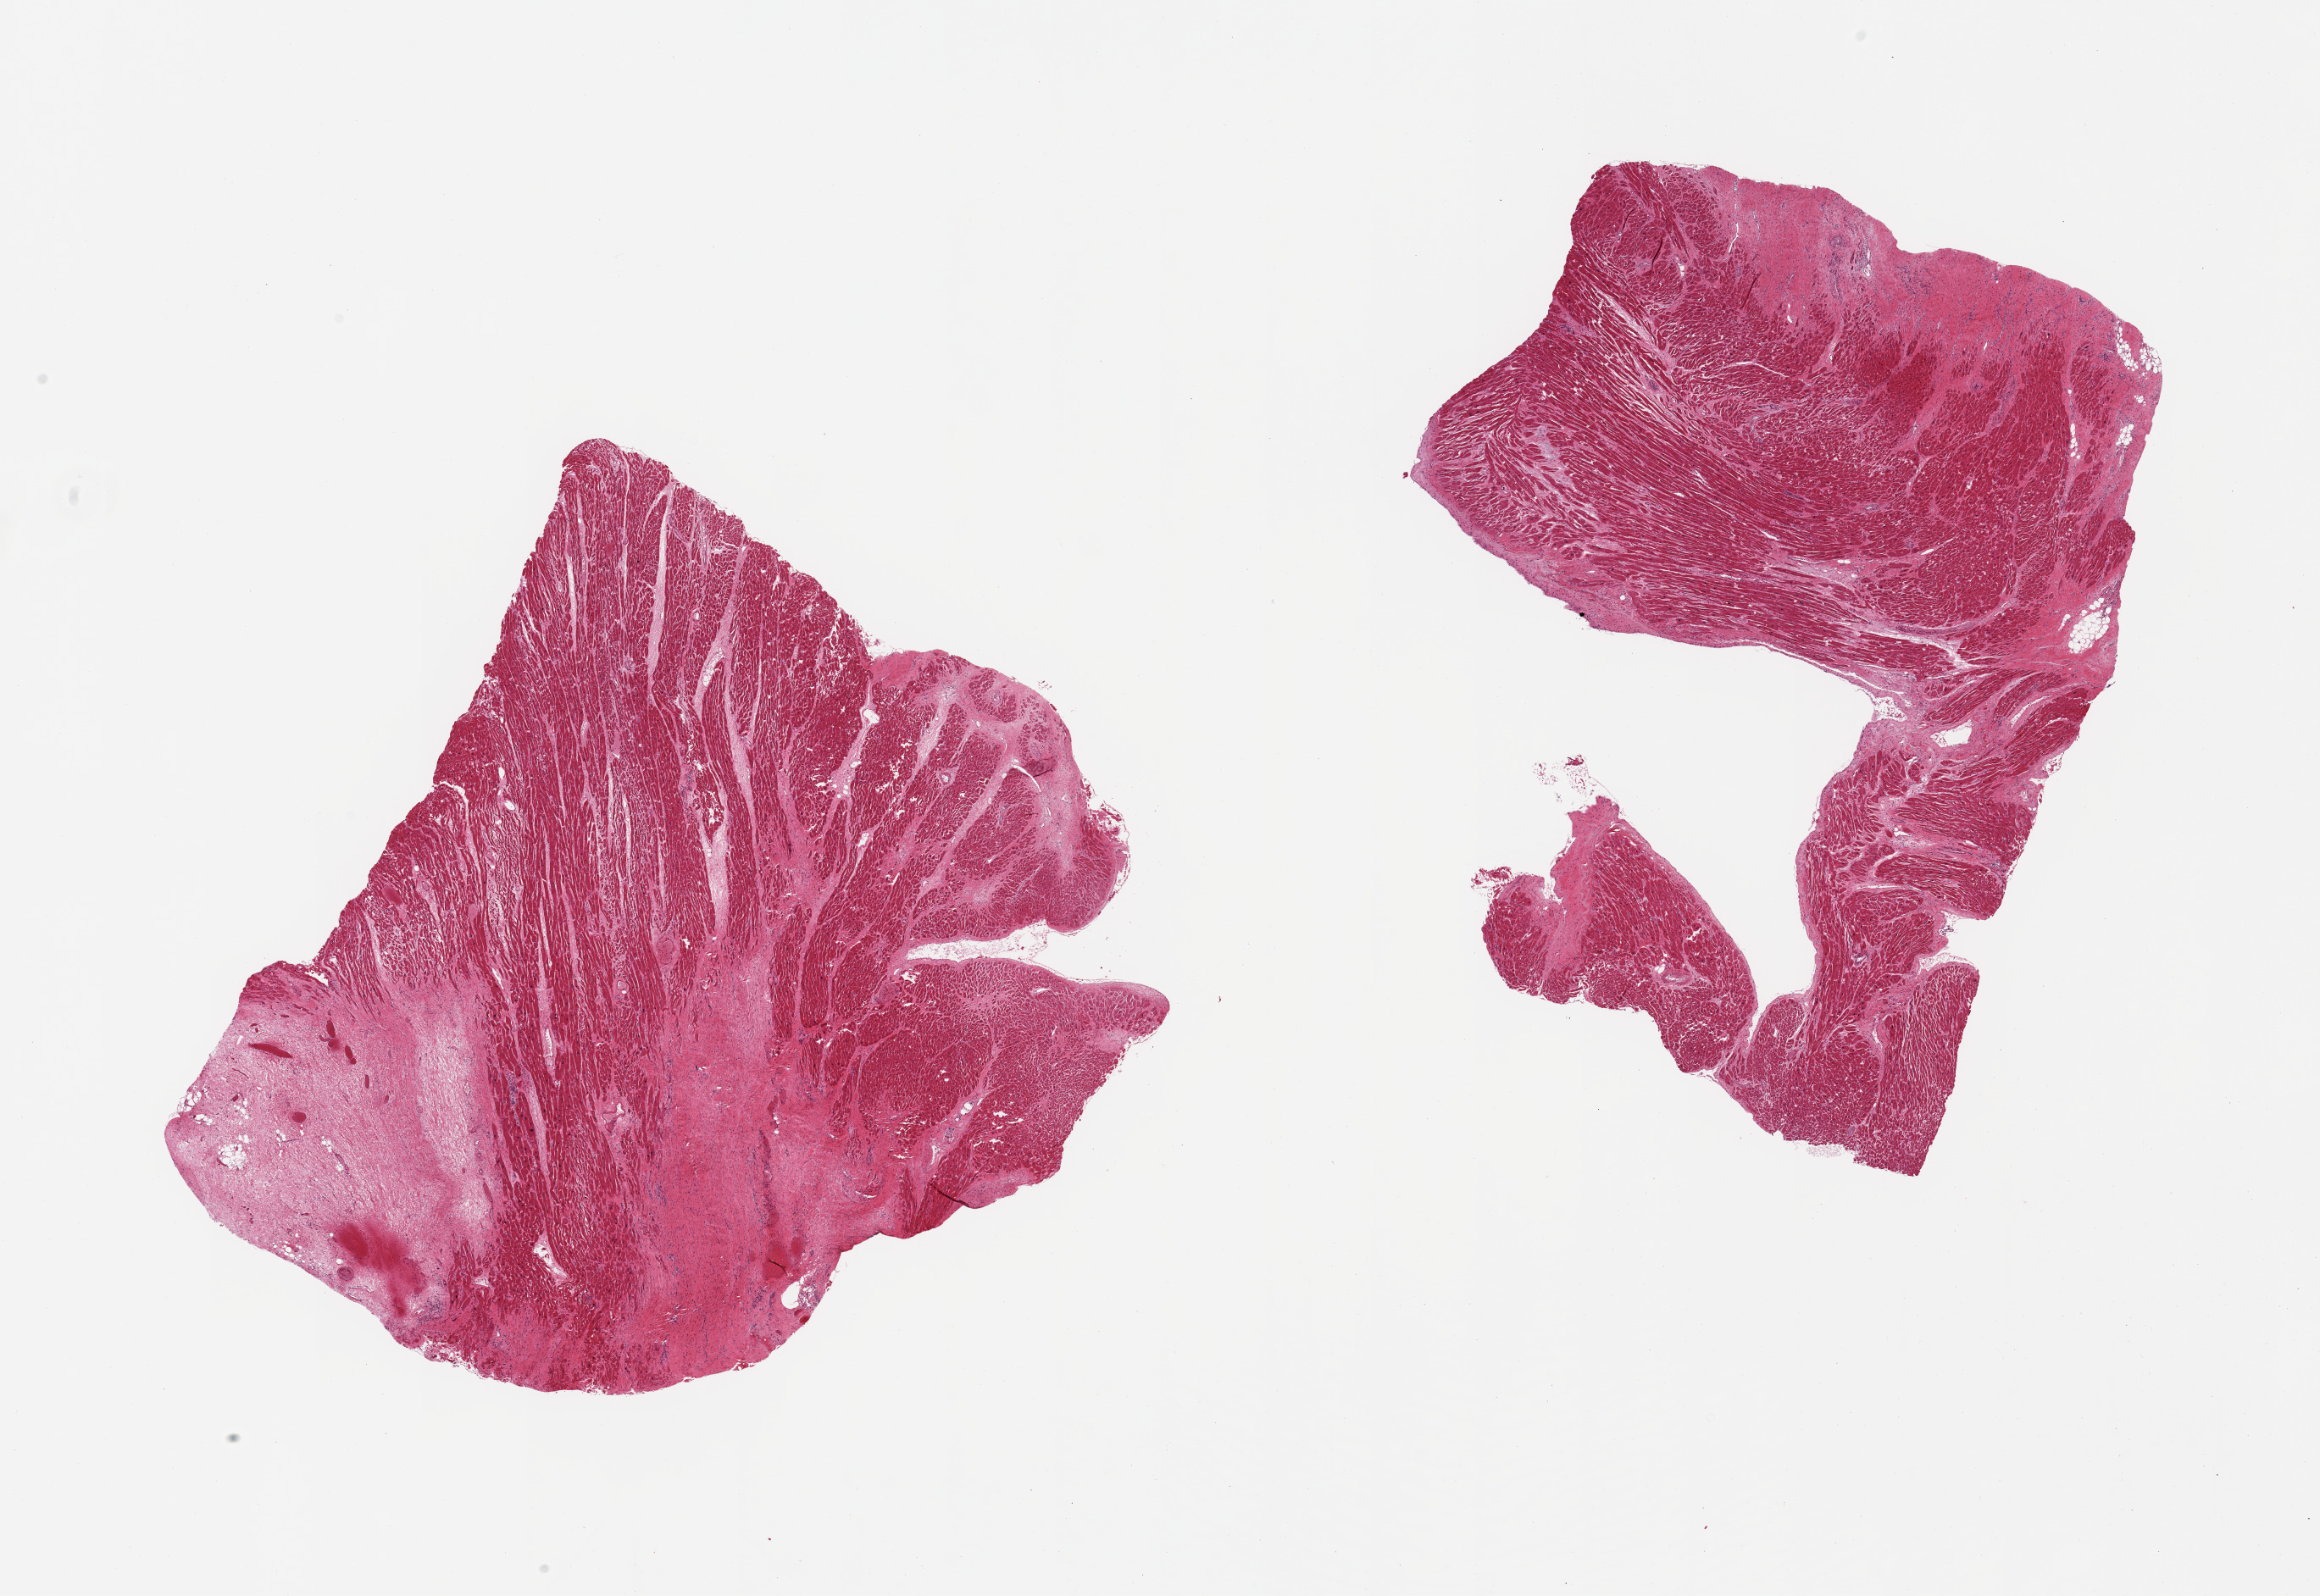
H&E whole-slide image — a low-resolution overview of the entire scanned area, about 21.7 x 14.9 mm; PAXgene-fixed, paraffin-embedded tissue; section of heart (target tissue); donor tissue sample. Male donor.
Reviewer comment on this tissue sample: 2 pieces, multiple healed infarcts.